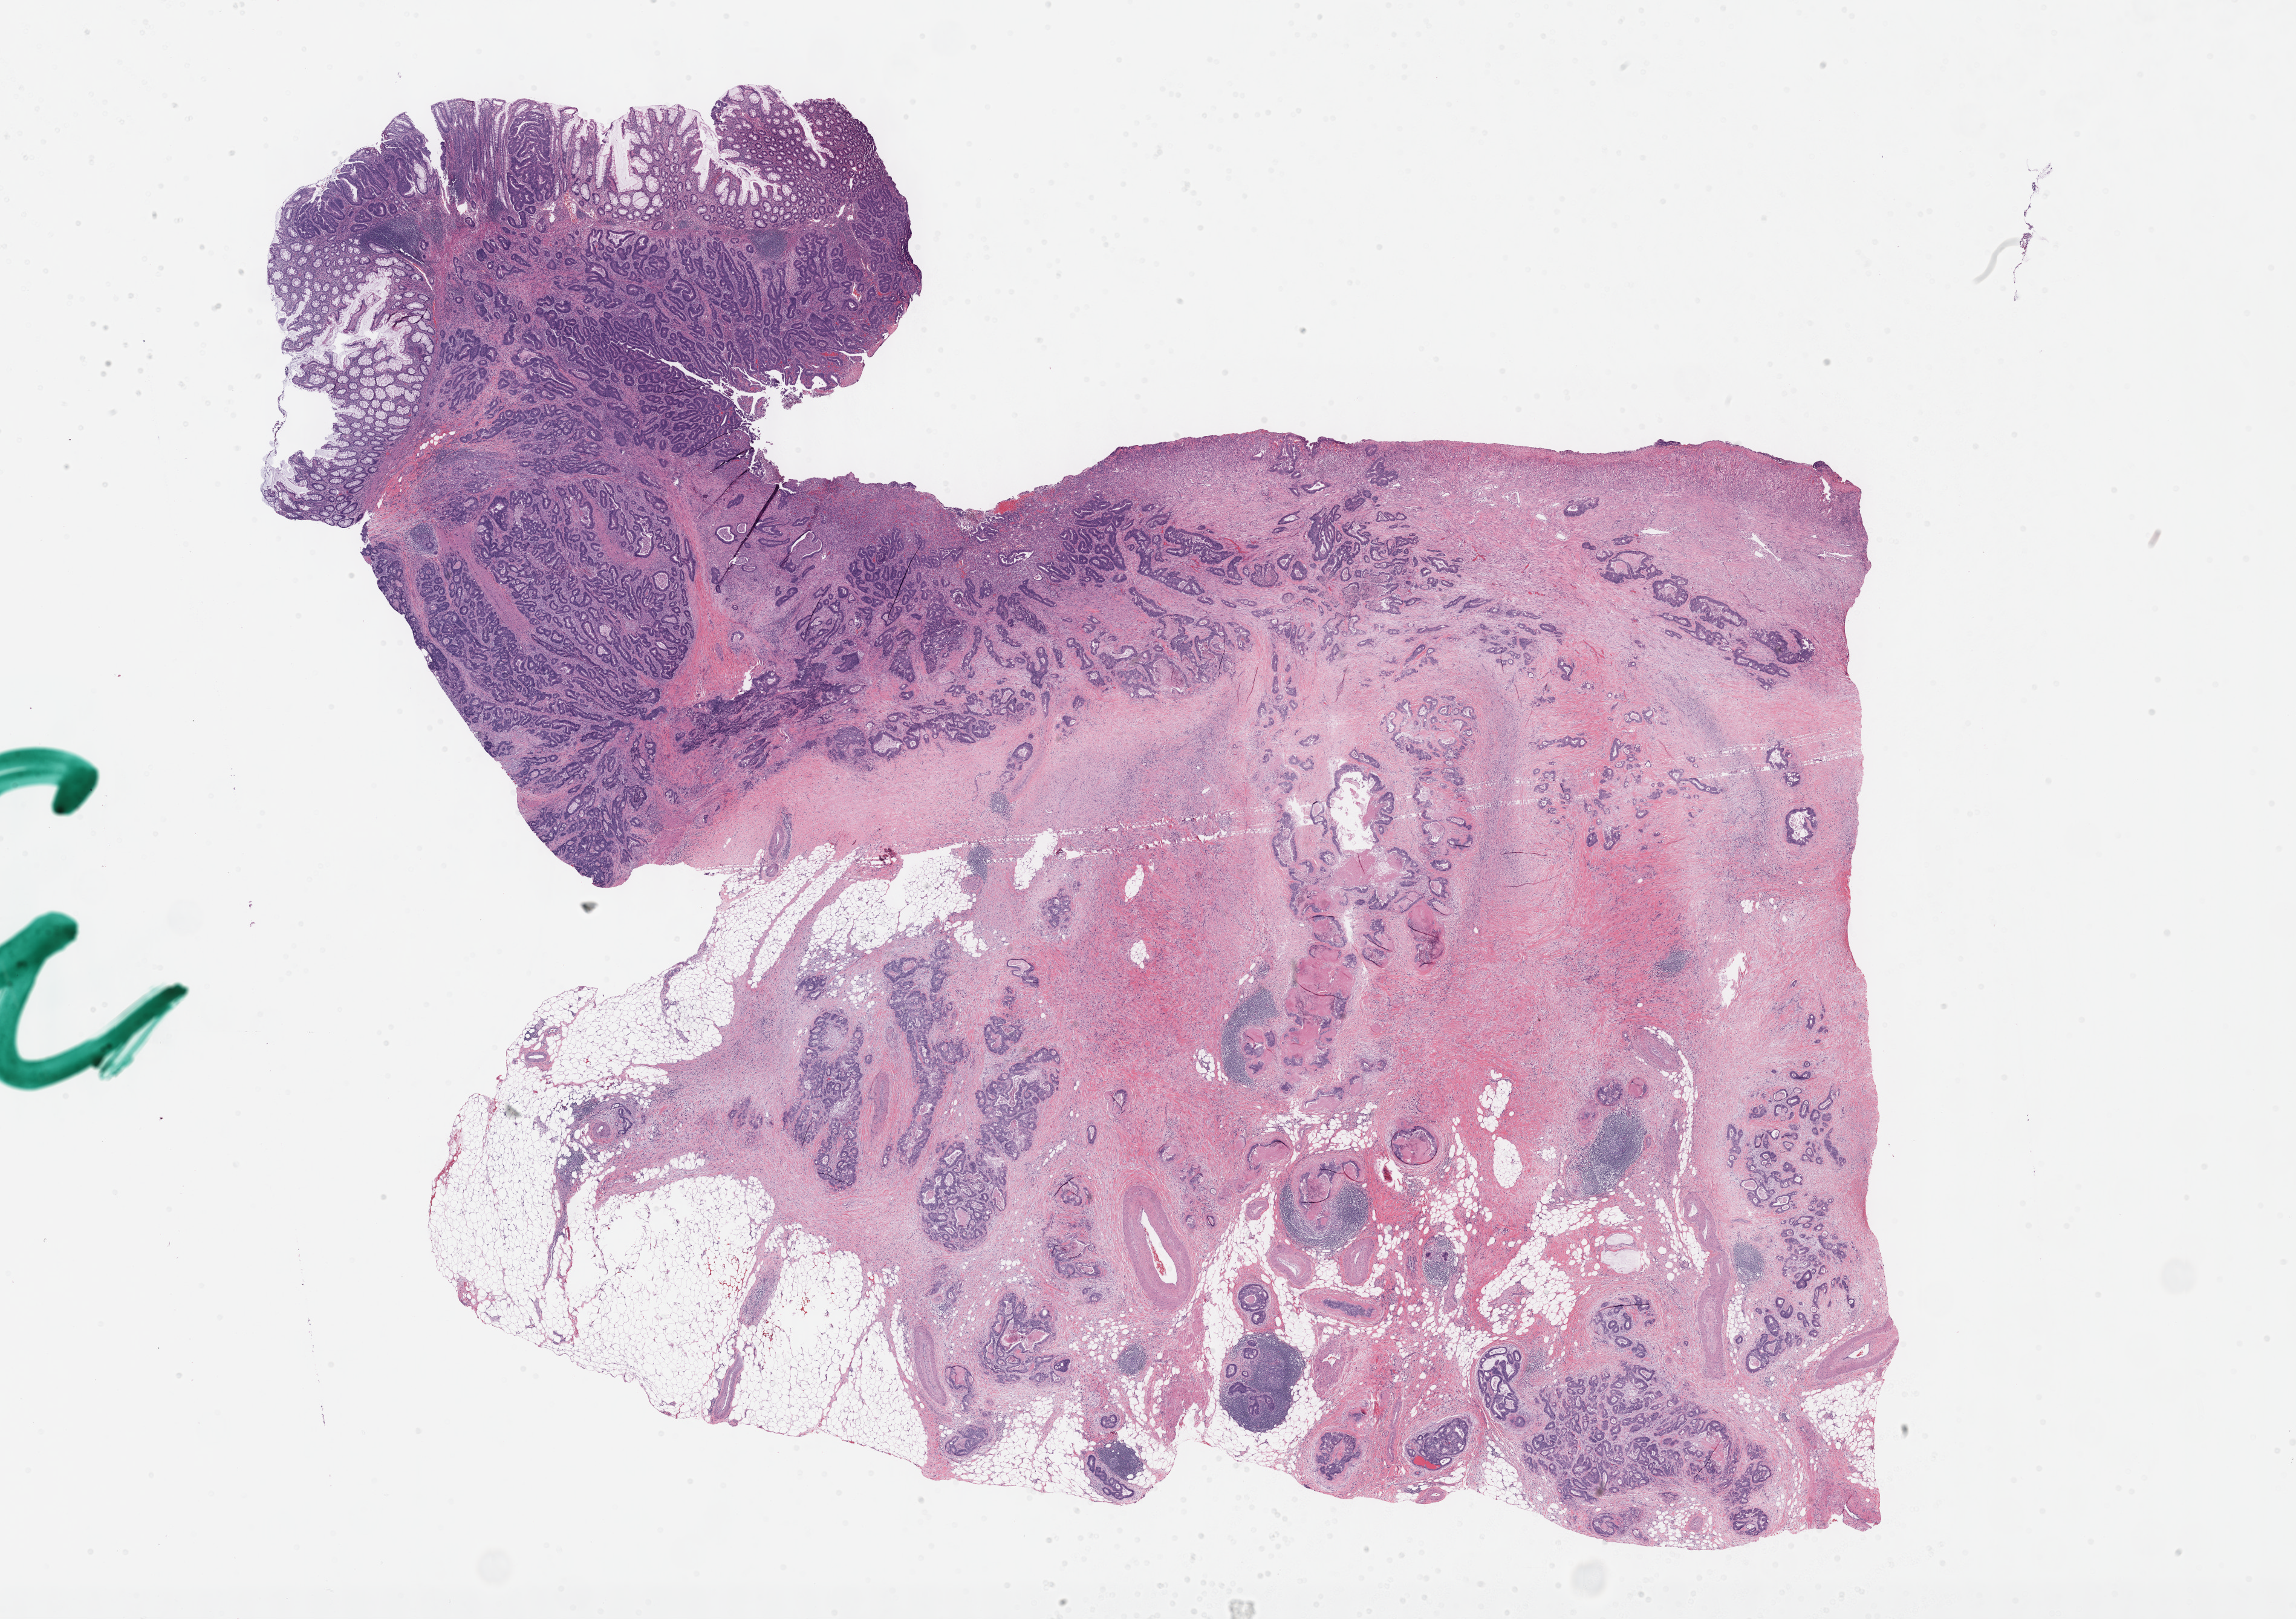
Digitized H&E tissue section (whole slide) — shown as a low-resolution overview of the whole scanned area (about 30.7 x 21.6 mm, slide scanned at 40x). Formalin-fixed paraffin-embedded (FFPE) diagnostic section. Sample: primary tumour, colon. Male, age 71 years at initial diagnosis.
Pathologic diagnosis: Adenocarcinoma, NOS (rectosigmoid junction).